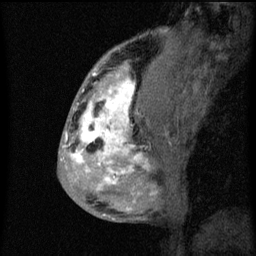
Breast MRI (dynamic contrast-enhanced), one sagittal slice; dynamic contrast-enhanced series, image 2 of 3 at this slice position (ordered by acquisition); 1.5 T; TE 4.2 ms, TR 8 ms; 2 mm slice thickness; 256 × 256 image matrix, field of view 180 × 180 mm. Female patient, age 50 years.
Annotated regions visible in this slice (semi-automatic segmentation, software-assisted and operator-edited):
- analysis volume of interest (the breast-tissue region the enhancement analysis was run in; not a lesion): bounding box (x1, y1, x2, y2) in pixels: (66, 64, 141, 187)
- tumour enhancement mask (voxels above the 70 % enhancement threshold inside the analysis volume of interest): (66, 72, 141, 185)